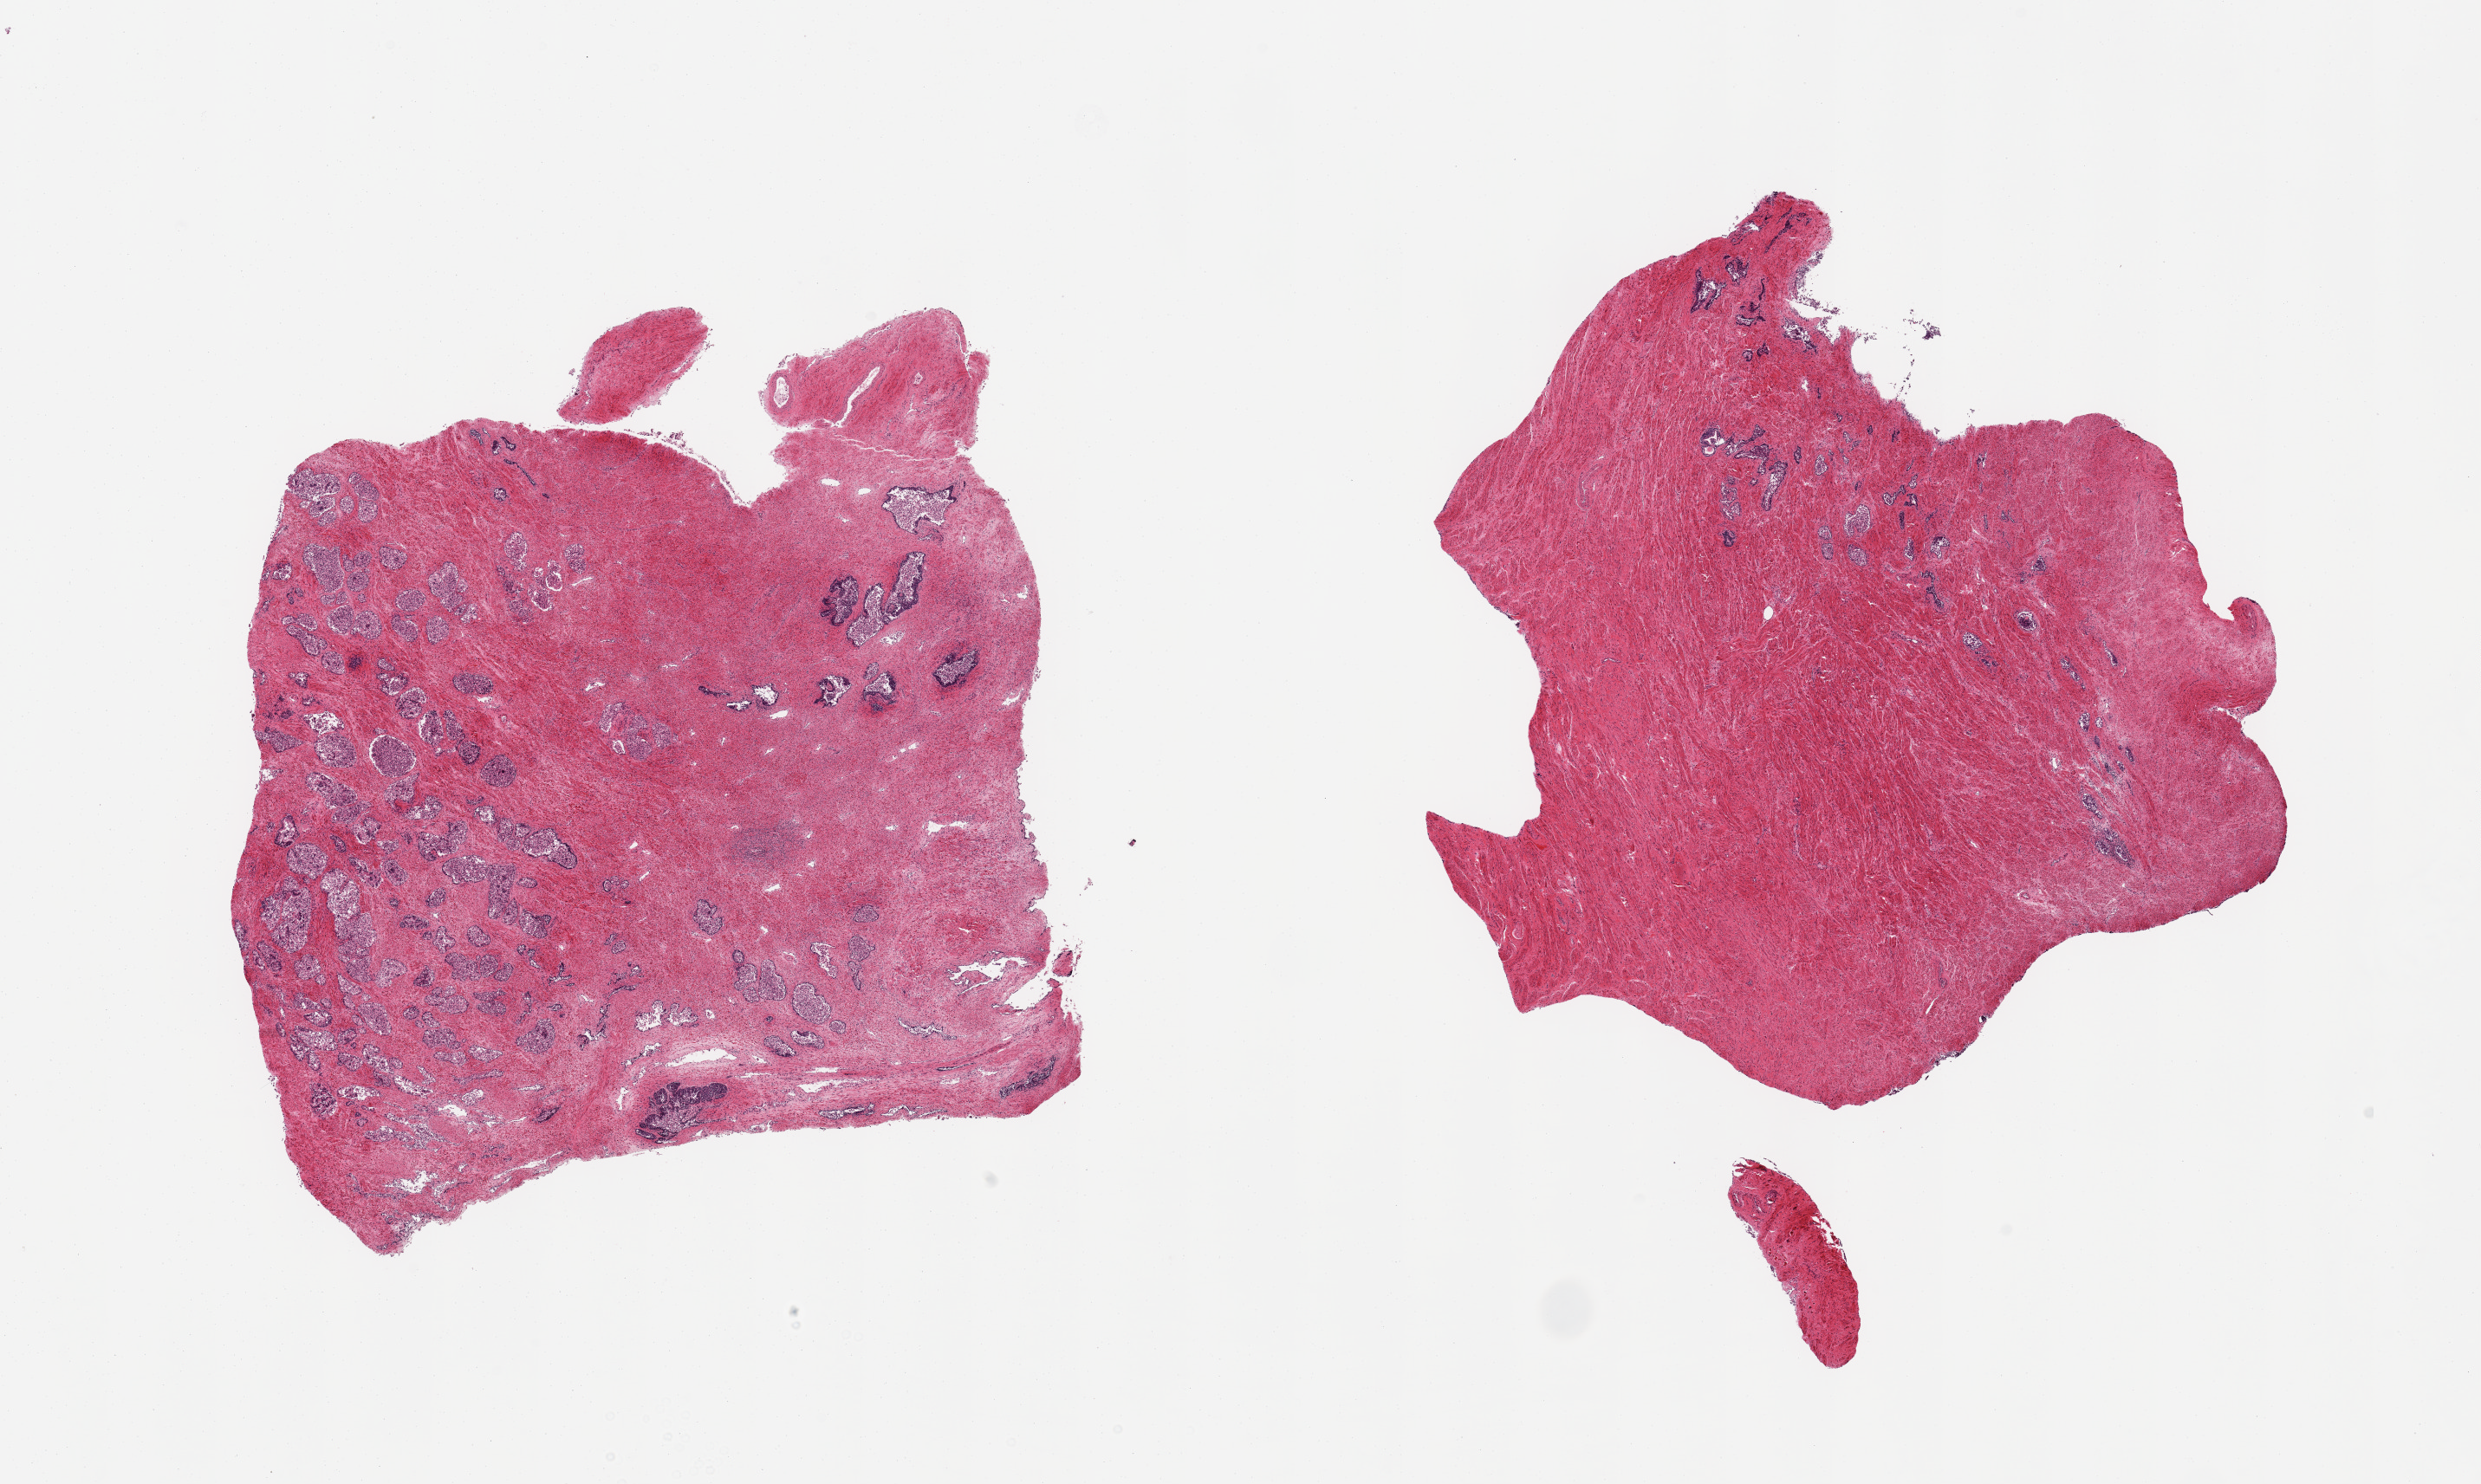
Whole-slide image, hematoxylin and eosin (H&E) stain — a low-resolution overview of the entire scanned area, about 22.6 x 13.5 mm (slide scanned at 20x); PAXgene-fixed, paraffin-embedded tissue; section of prostate (target tissue); tissue donor sample. Donor sex: male.
Pathologist's review note for this sample: 2 pieces; glands autolyzed, stroma intact.